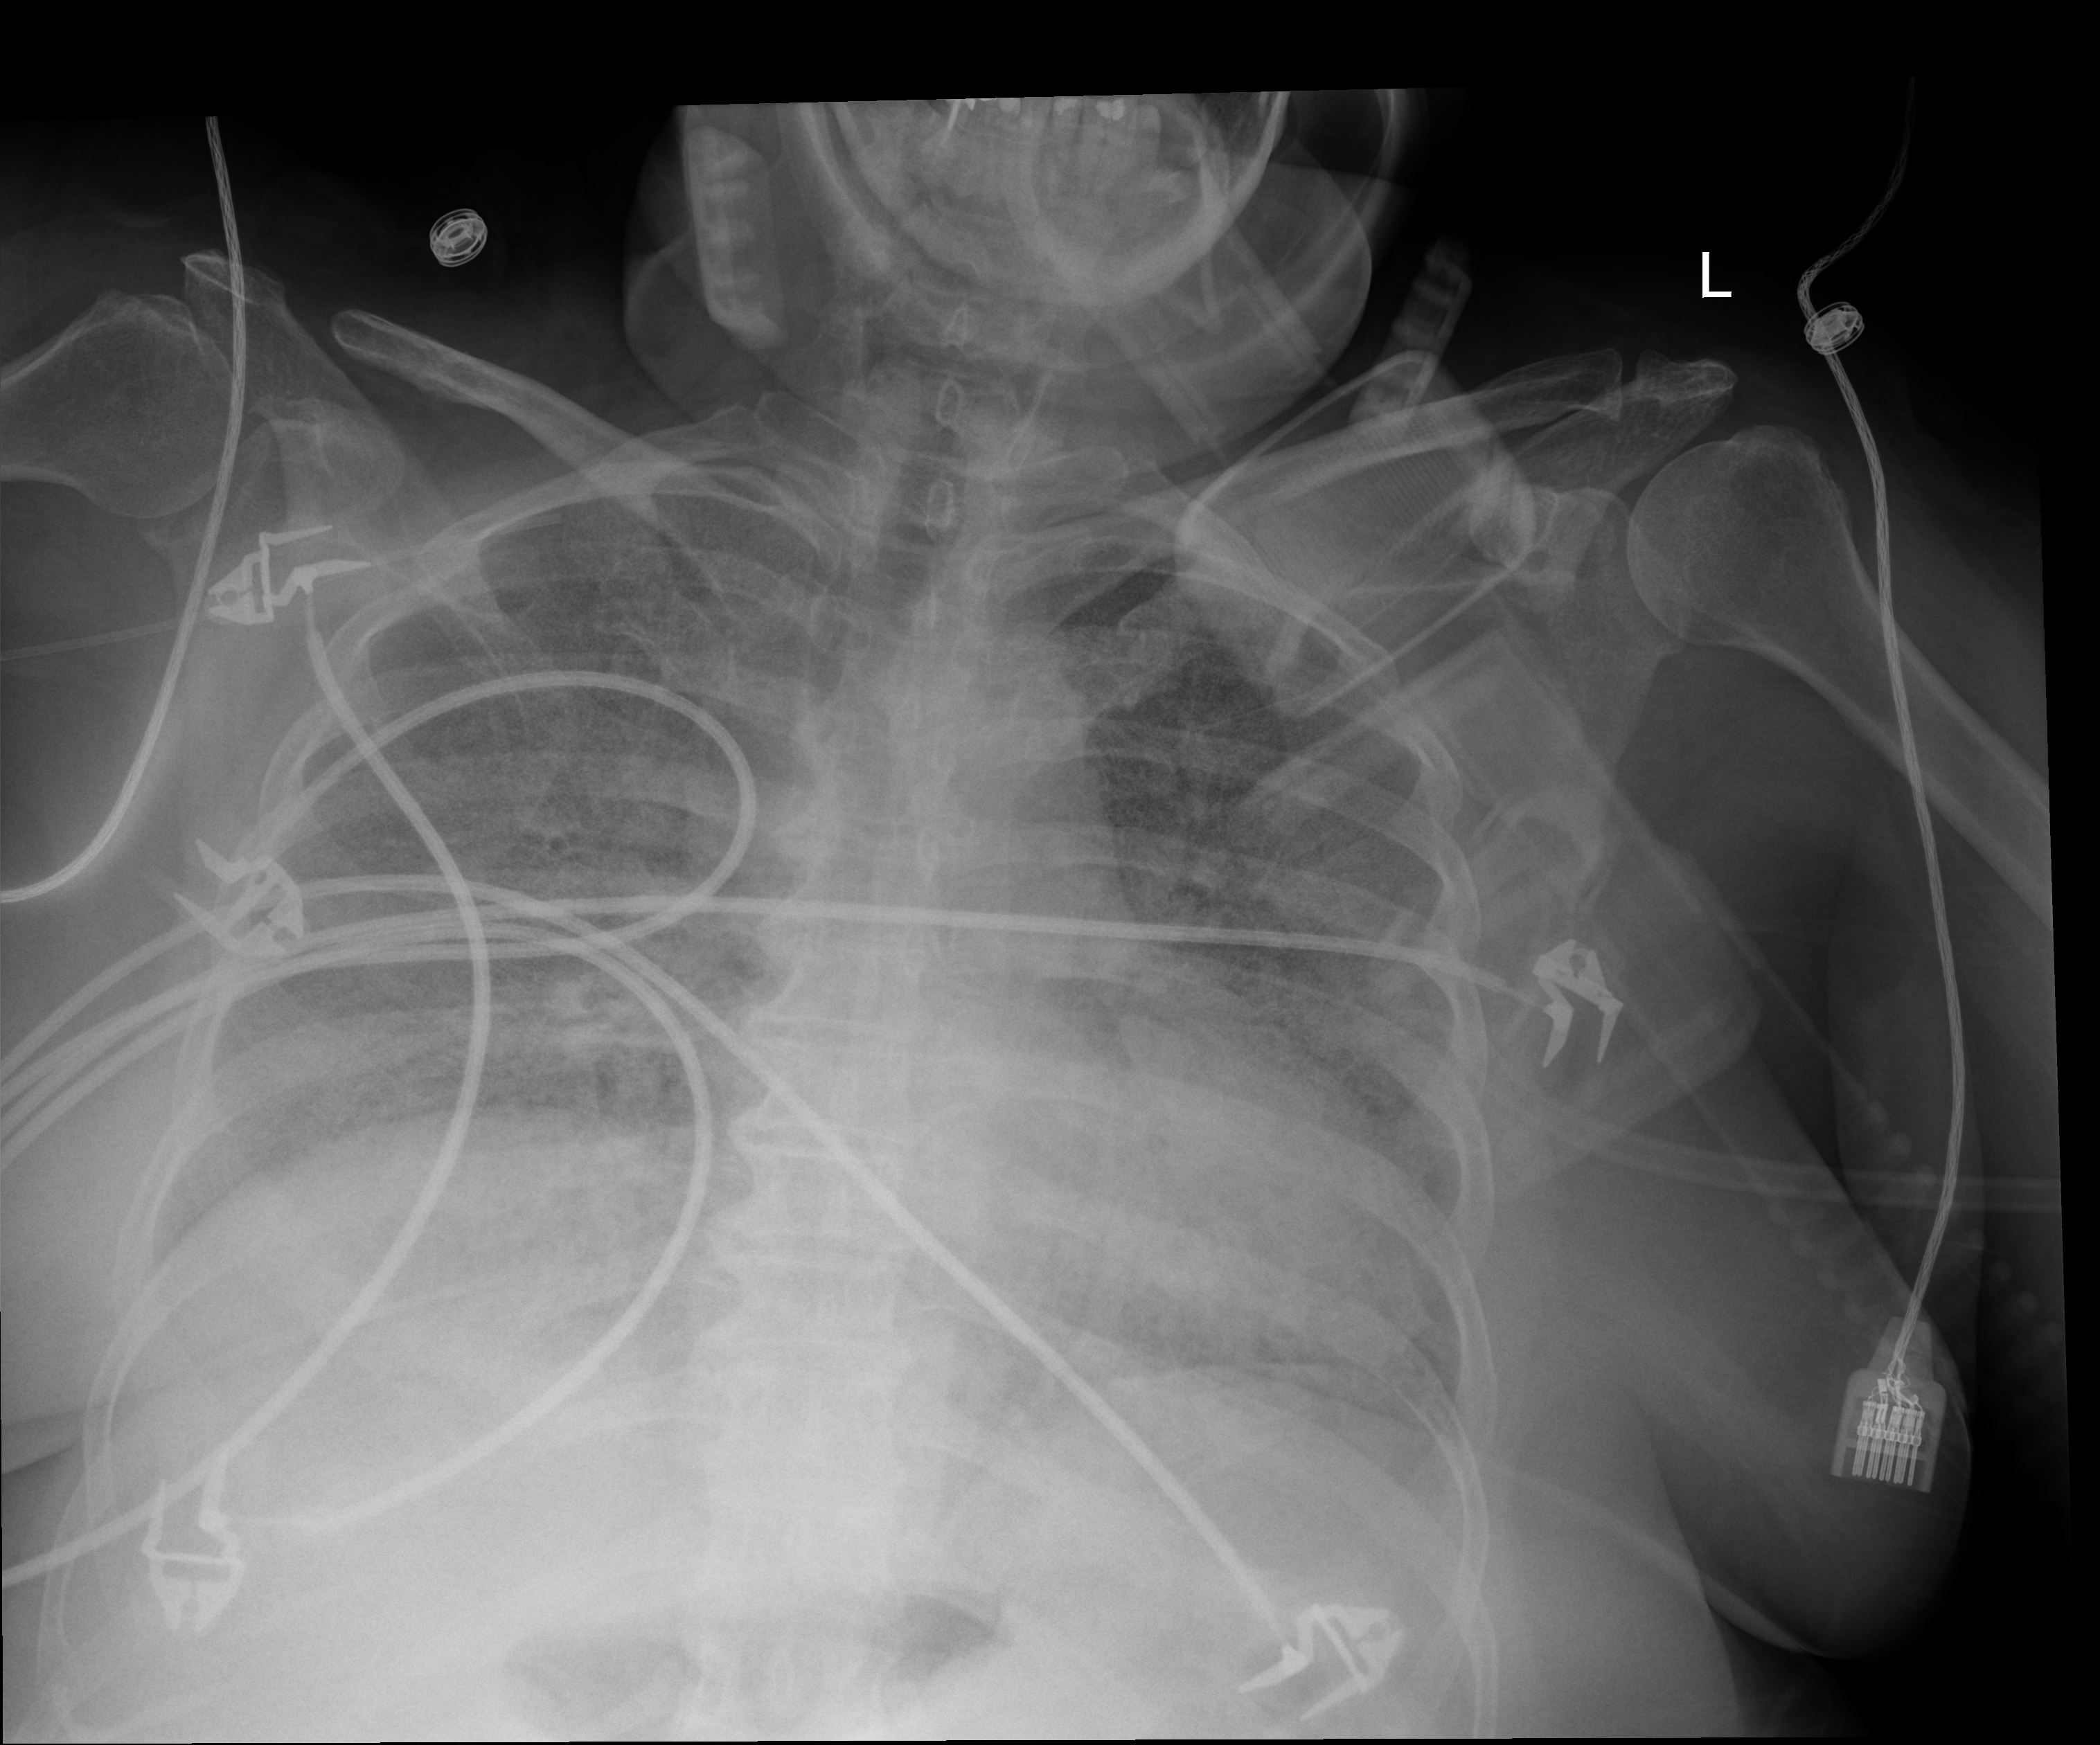
Portable chest radiograph, anteroposterior (AP) projection. Female patient hospitalised with COVID-19, age 60–74 years.
Admission-level facts for this patient (not findings on this image; timing relative to this image not recorded):
- mechanically ventilated during this hospital stay: yes
- other chronic lung disease (admission record): no
- admitted to intensive care during this hospital stay: yes